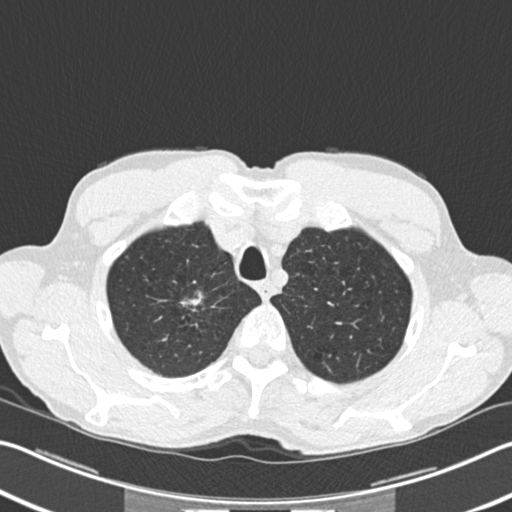
Low-dose screening chest CT, one axial slice. Slice 188 of 220 in the series (ordered by position). Reconstruction kernel B30f. Lung window (W 1500 / L -600 HU). 512 × 512 image matrix.
Annotated regions visible in this slice (outlined manually by an expert reader):
- lesion 1 (tumor, upper lobe of right lung): box from (x=183, y=298) to (x=201, y=306) px